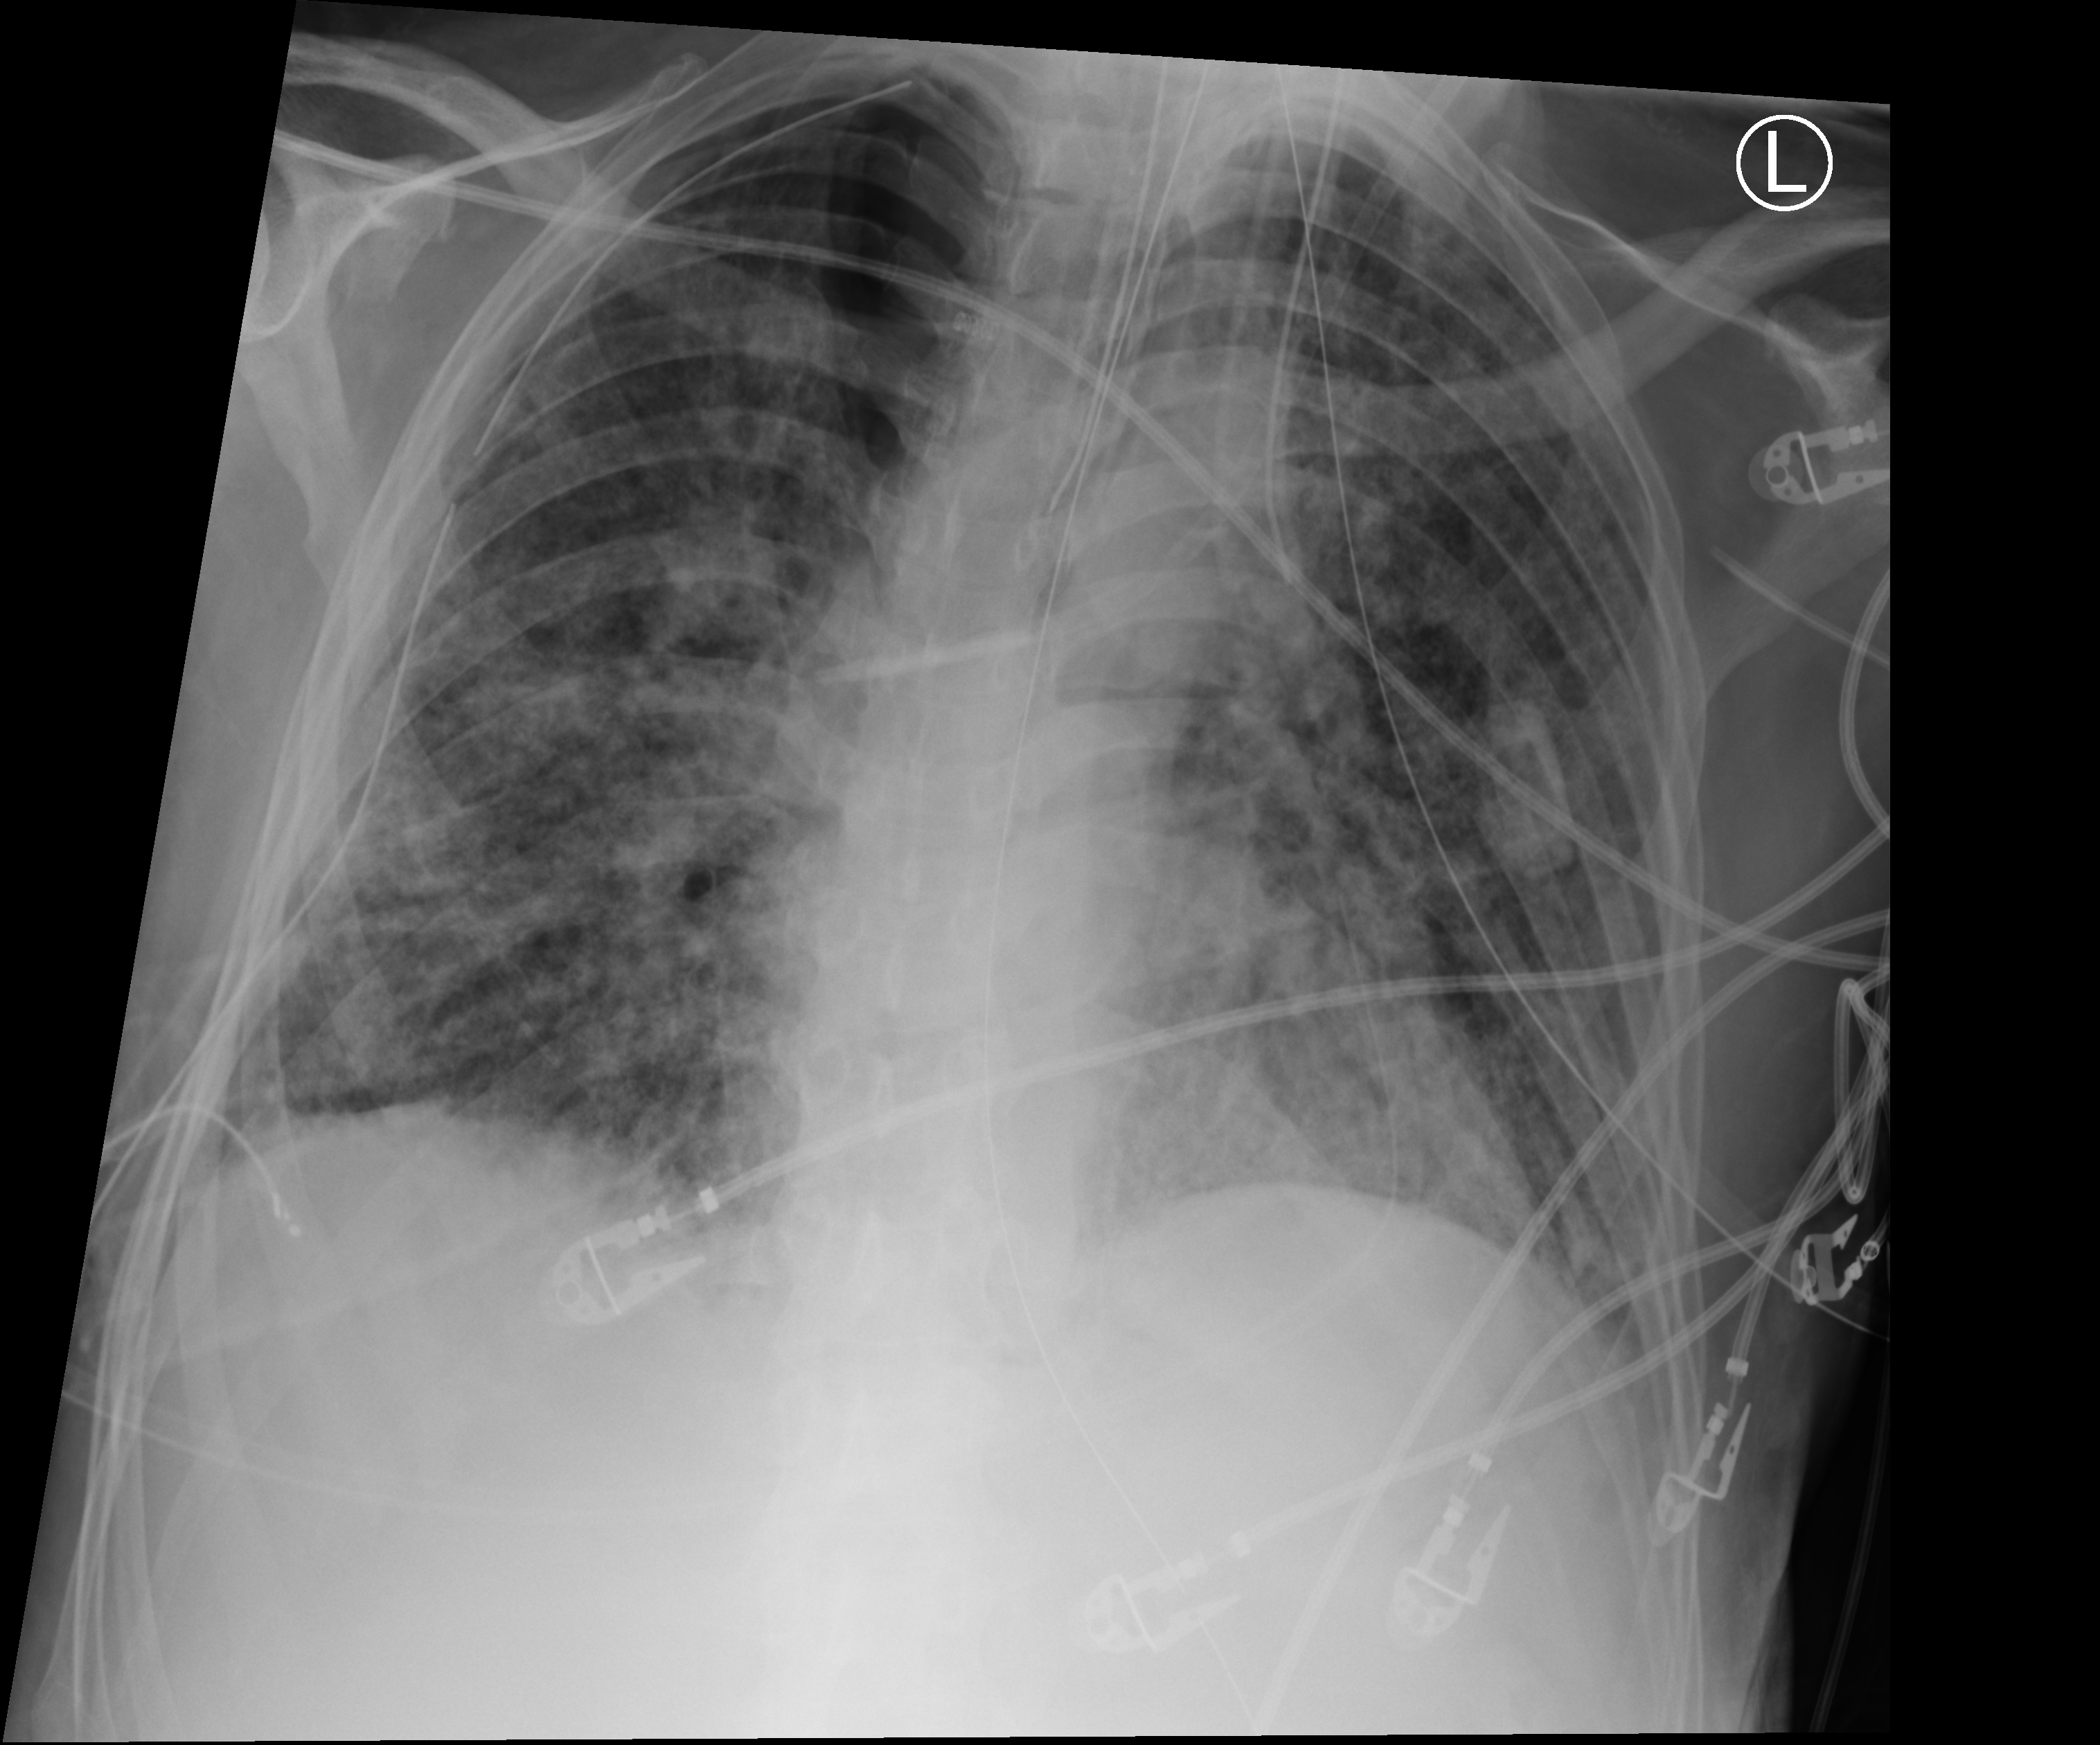
Chest X-ray (portable); anteroposterior (AP) projection. Patient hospitalised with COVID-19; male, aged 60–74 years.
From the hospital-stay record, not from the radiograph (when in the stay this image was taken is not recorded):
- smoking status (admission record): never
- admitted to intensive care during this hospital stay: yes
- length of hospital stay: 65 days